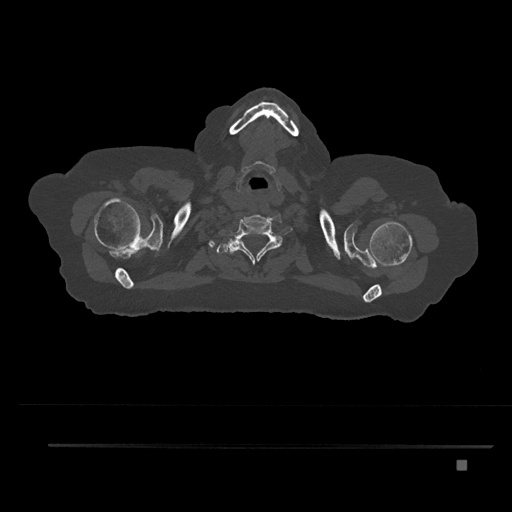
CT including the spine, one axial slice. Position 721 of 797 along the scan axis. Bone window (W 1800 / L 400 HU). 0.5 mm slice thickness. 512 × 512 image matrix. Female patient, age 76 years. From the clinical record (not read from this slice): primary cancer: lung; vertebrae with lytic lesions (as recorded): T11, L3.
Structures marked on this image (semi-automatic segmentation, software-assisted and operator-edited):
- T1 vertebra: bounding box [x1, y1, x2, y2] px = [222, 241, 260, 258]